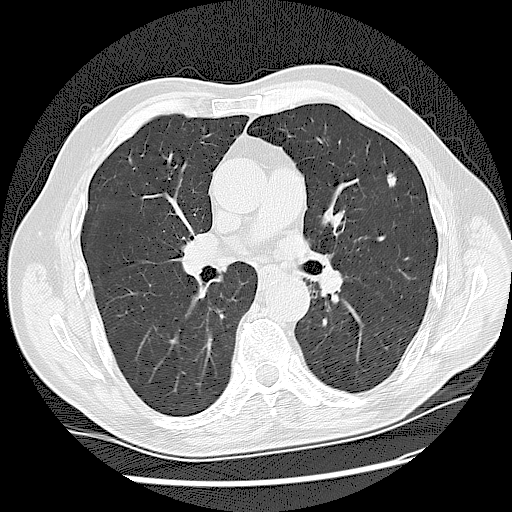
Low-dose screening chest CT, one axial slice. Slice 87 of 159 in the series (ordered by position). Reconstruction kernel LUNG. 120 kVp. Lung window (W 1500 / L -600 HU). 512 × 512 image matrix.
Structures marked on this image (manually delineated by an expert):
- lesion 1 (tumor, upper lobe of left lung): bounding box [x1, y1, x2, y2] px = [387, 174, 396, 187]